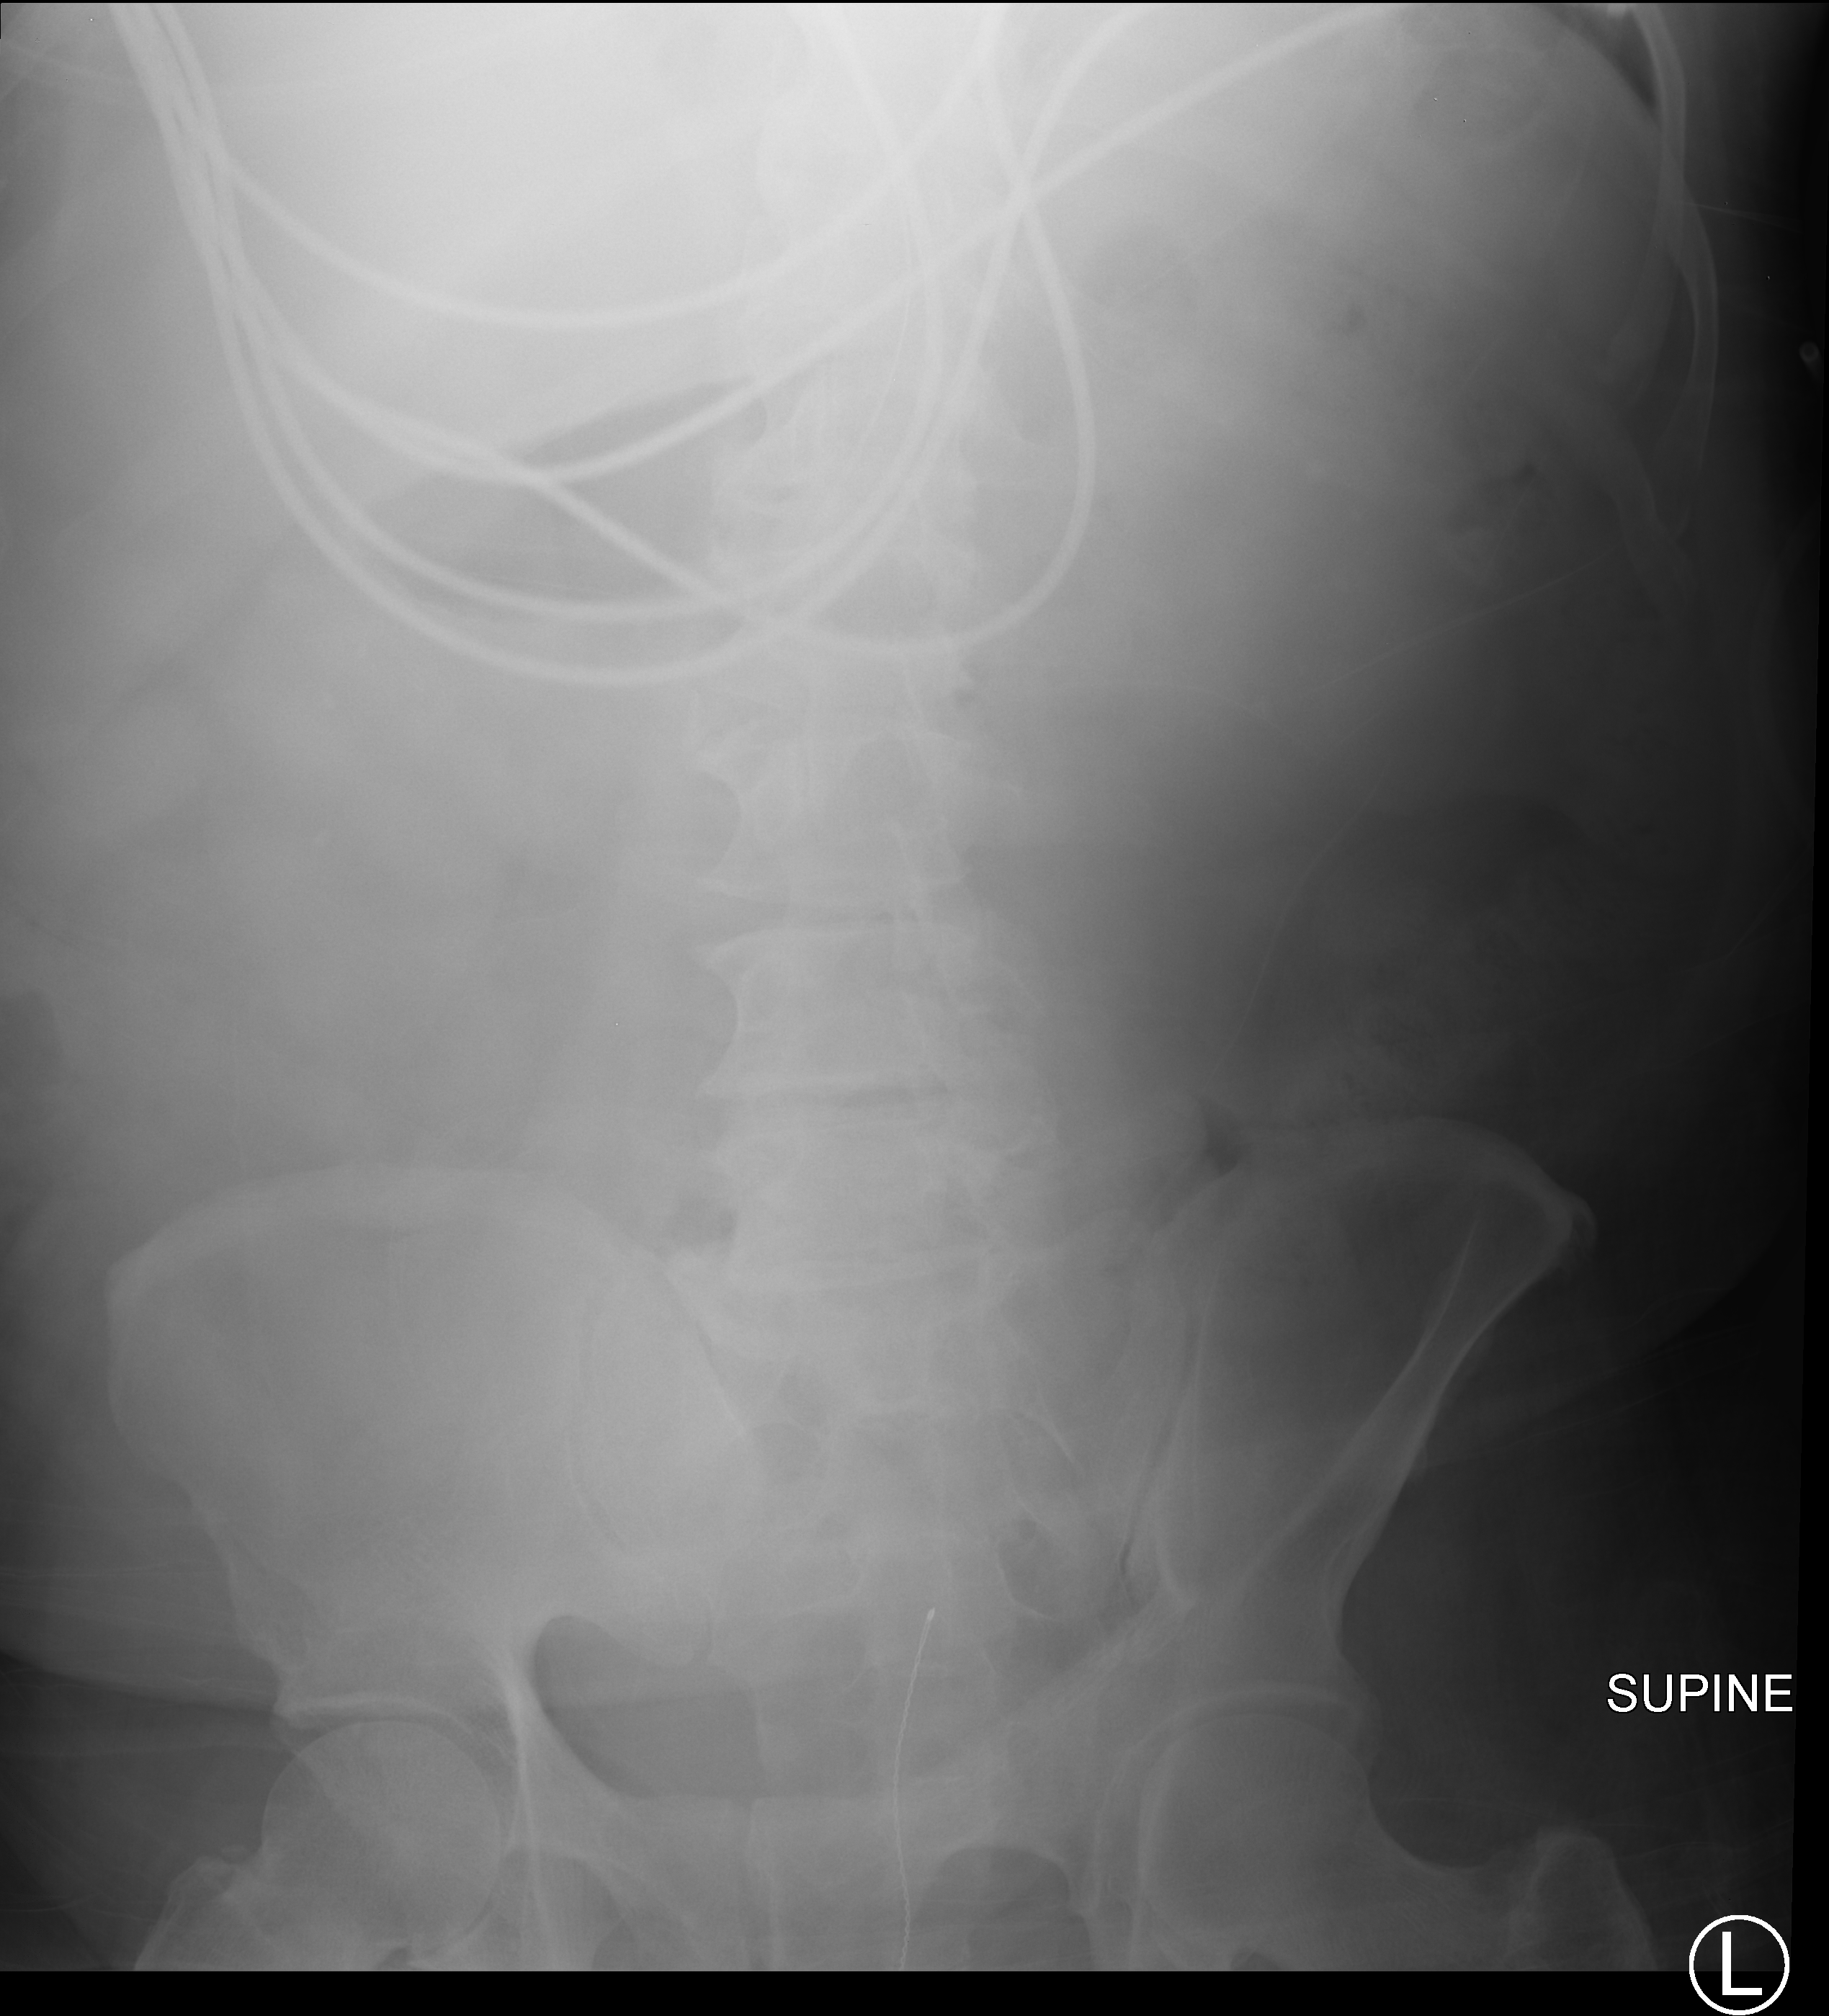
Abdomen X-ray (portable), anteroposterior (AP) projection. Patient hospitalised with COVID-19; male, aged 60–74 years.
Hospital-stay facts (about this admission, not read from this image; timing relative to this image not recorded): mechanically ventilated during this hospital stay: yes.